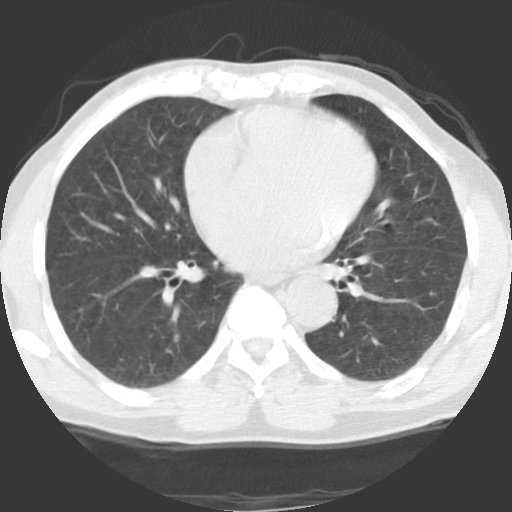
Axial slice from a low-dose chest CT screening exam, baseline screening round, lung window (W 1500 / L -600 HU), 2.5 mm slice thickness, slice 40 of 109 in the series, 512 × 512 image matrix. Male participant, aged 58 years at enrolment. Current smoker at enrolment.
• Expert-annotated lung lesion, bounding box (x1, y1, x2, y2) in pixels: (162, 327, 193, 355).
• The exam's reader record, not a measurement of the box and not confirmed to be the same lesion: non-calcified nodule or mass ≥4 mm, left upper lobe, 10 × 9 mm, poorly defined margins, ground glass attenuation.
• Note: the box lies in the patient's right hemithorax on this image, whereas the reader's record names the left lung; they may be different findings.
• Official screen result: positive, change unspecified: nodule(s) >= 4 mm or enlarging nodule(s), mass(es), or other non-specific abnormalities suspicious for lung cancer.
• Participant outcome: lung cancer diagnosed 1023 days after this screen — adenocarcinoma, NOS, right lower lobe, poorly differentiated (G3), stage IIIA (AJCC 6th edition), 15 mm at pathology.